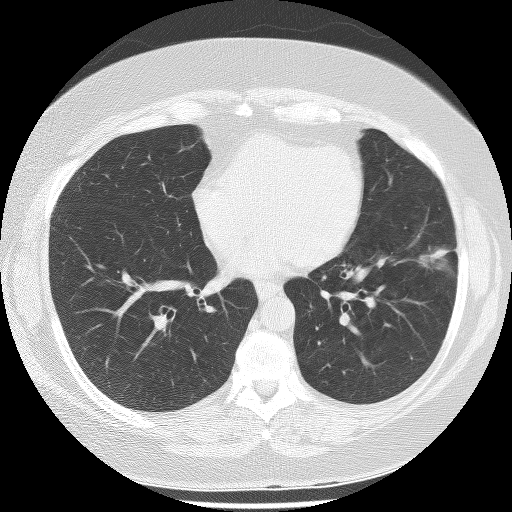
Low-dose screening chest CT, one axial slice; slice 108 of 233 in the series (ordered by position); reconstruction kernel BONE; 120 kVp; lung window (W 1500 / L -600 HU); 512 × 512 image matrix.
Annotated regions visible in this slice (expert manual segmentation):
- lesion 1 (tumor, lower lobe of left lung): box from (x=420, y=248) to (x=450, y=265) px